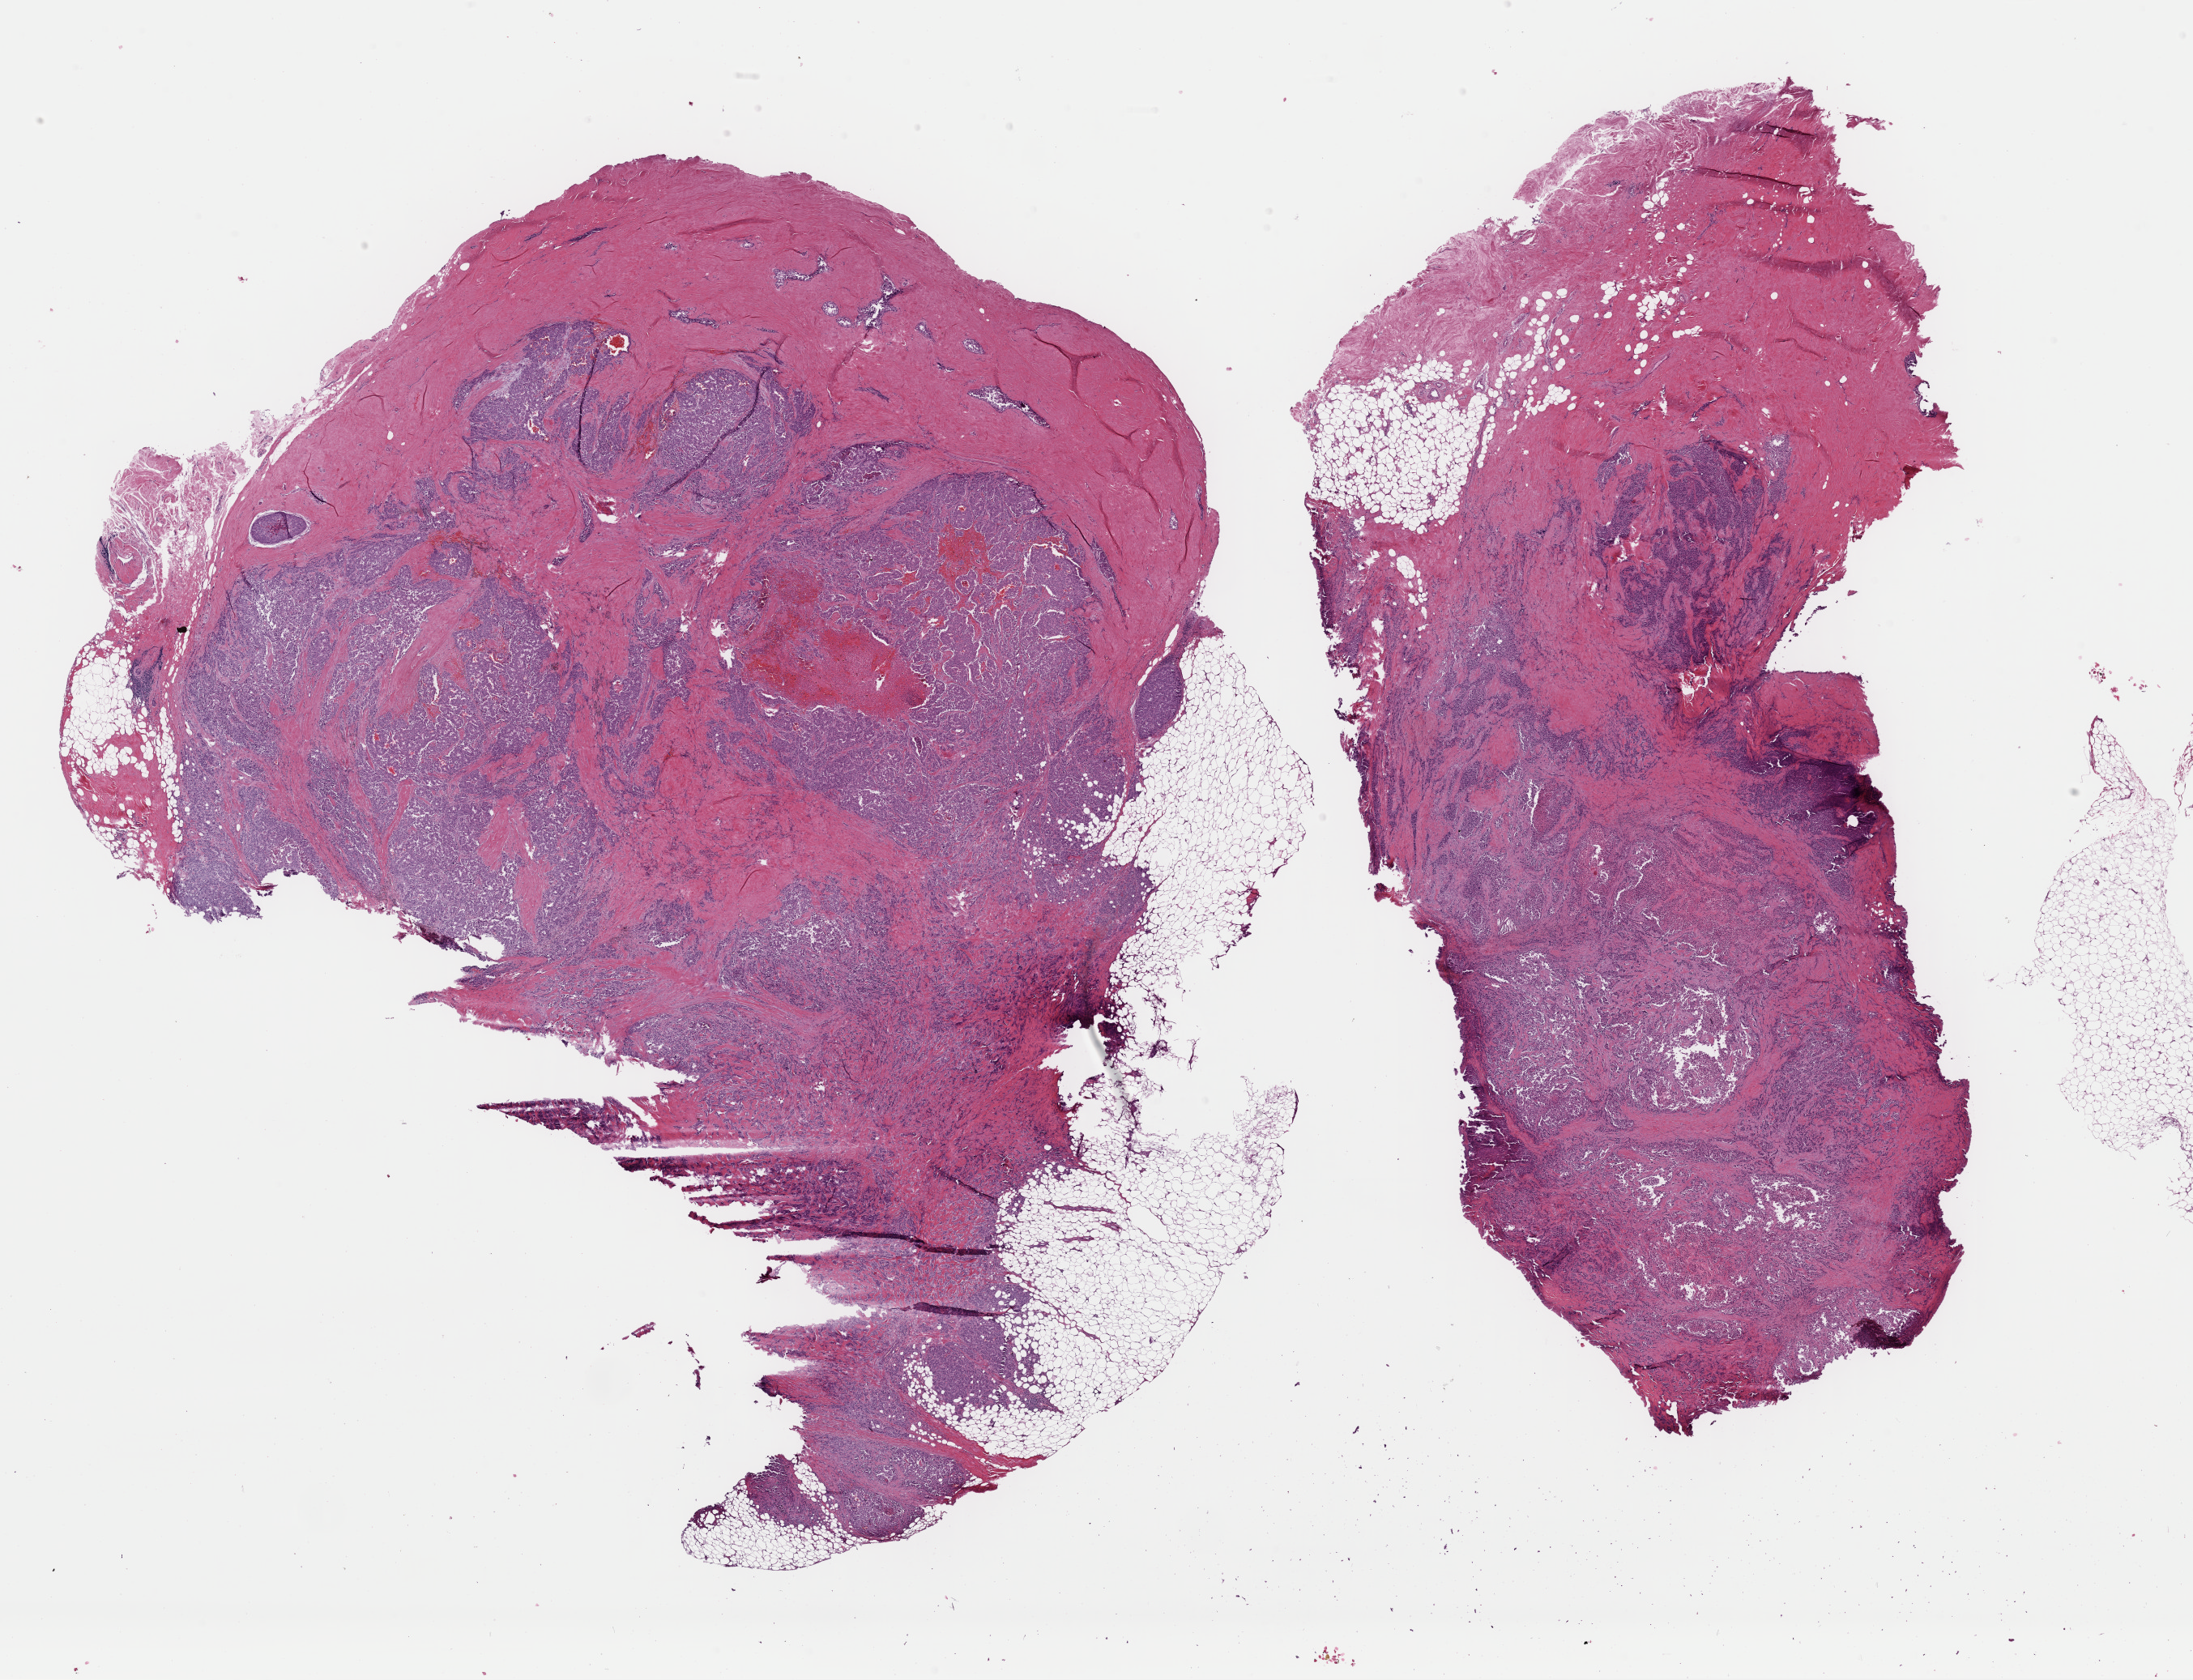
Digitized H&E tissue section (whole slide) — low-resolution overview of the scanned area, about 21.4 x 16.4 mm; formalin-fixed paraffin-embedded (FFPE) diagnostic section; breast, primary tumour sample. Female, age 54 years at initial diagnosis.
AJCC pathologic stage: IIA. Histologic diagnosis: Infiltrating duct carcinoma, NOS. Lymph nodes positive (case pathology): 0 of 15 examined. TNM: T2 N0 M0.